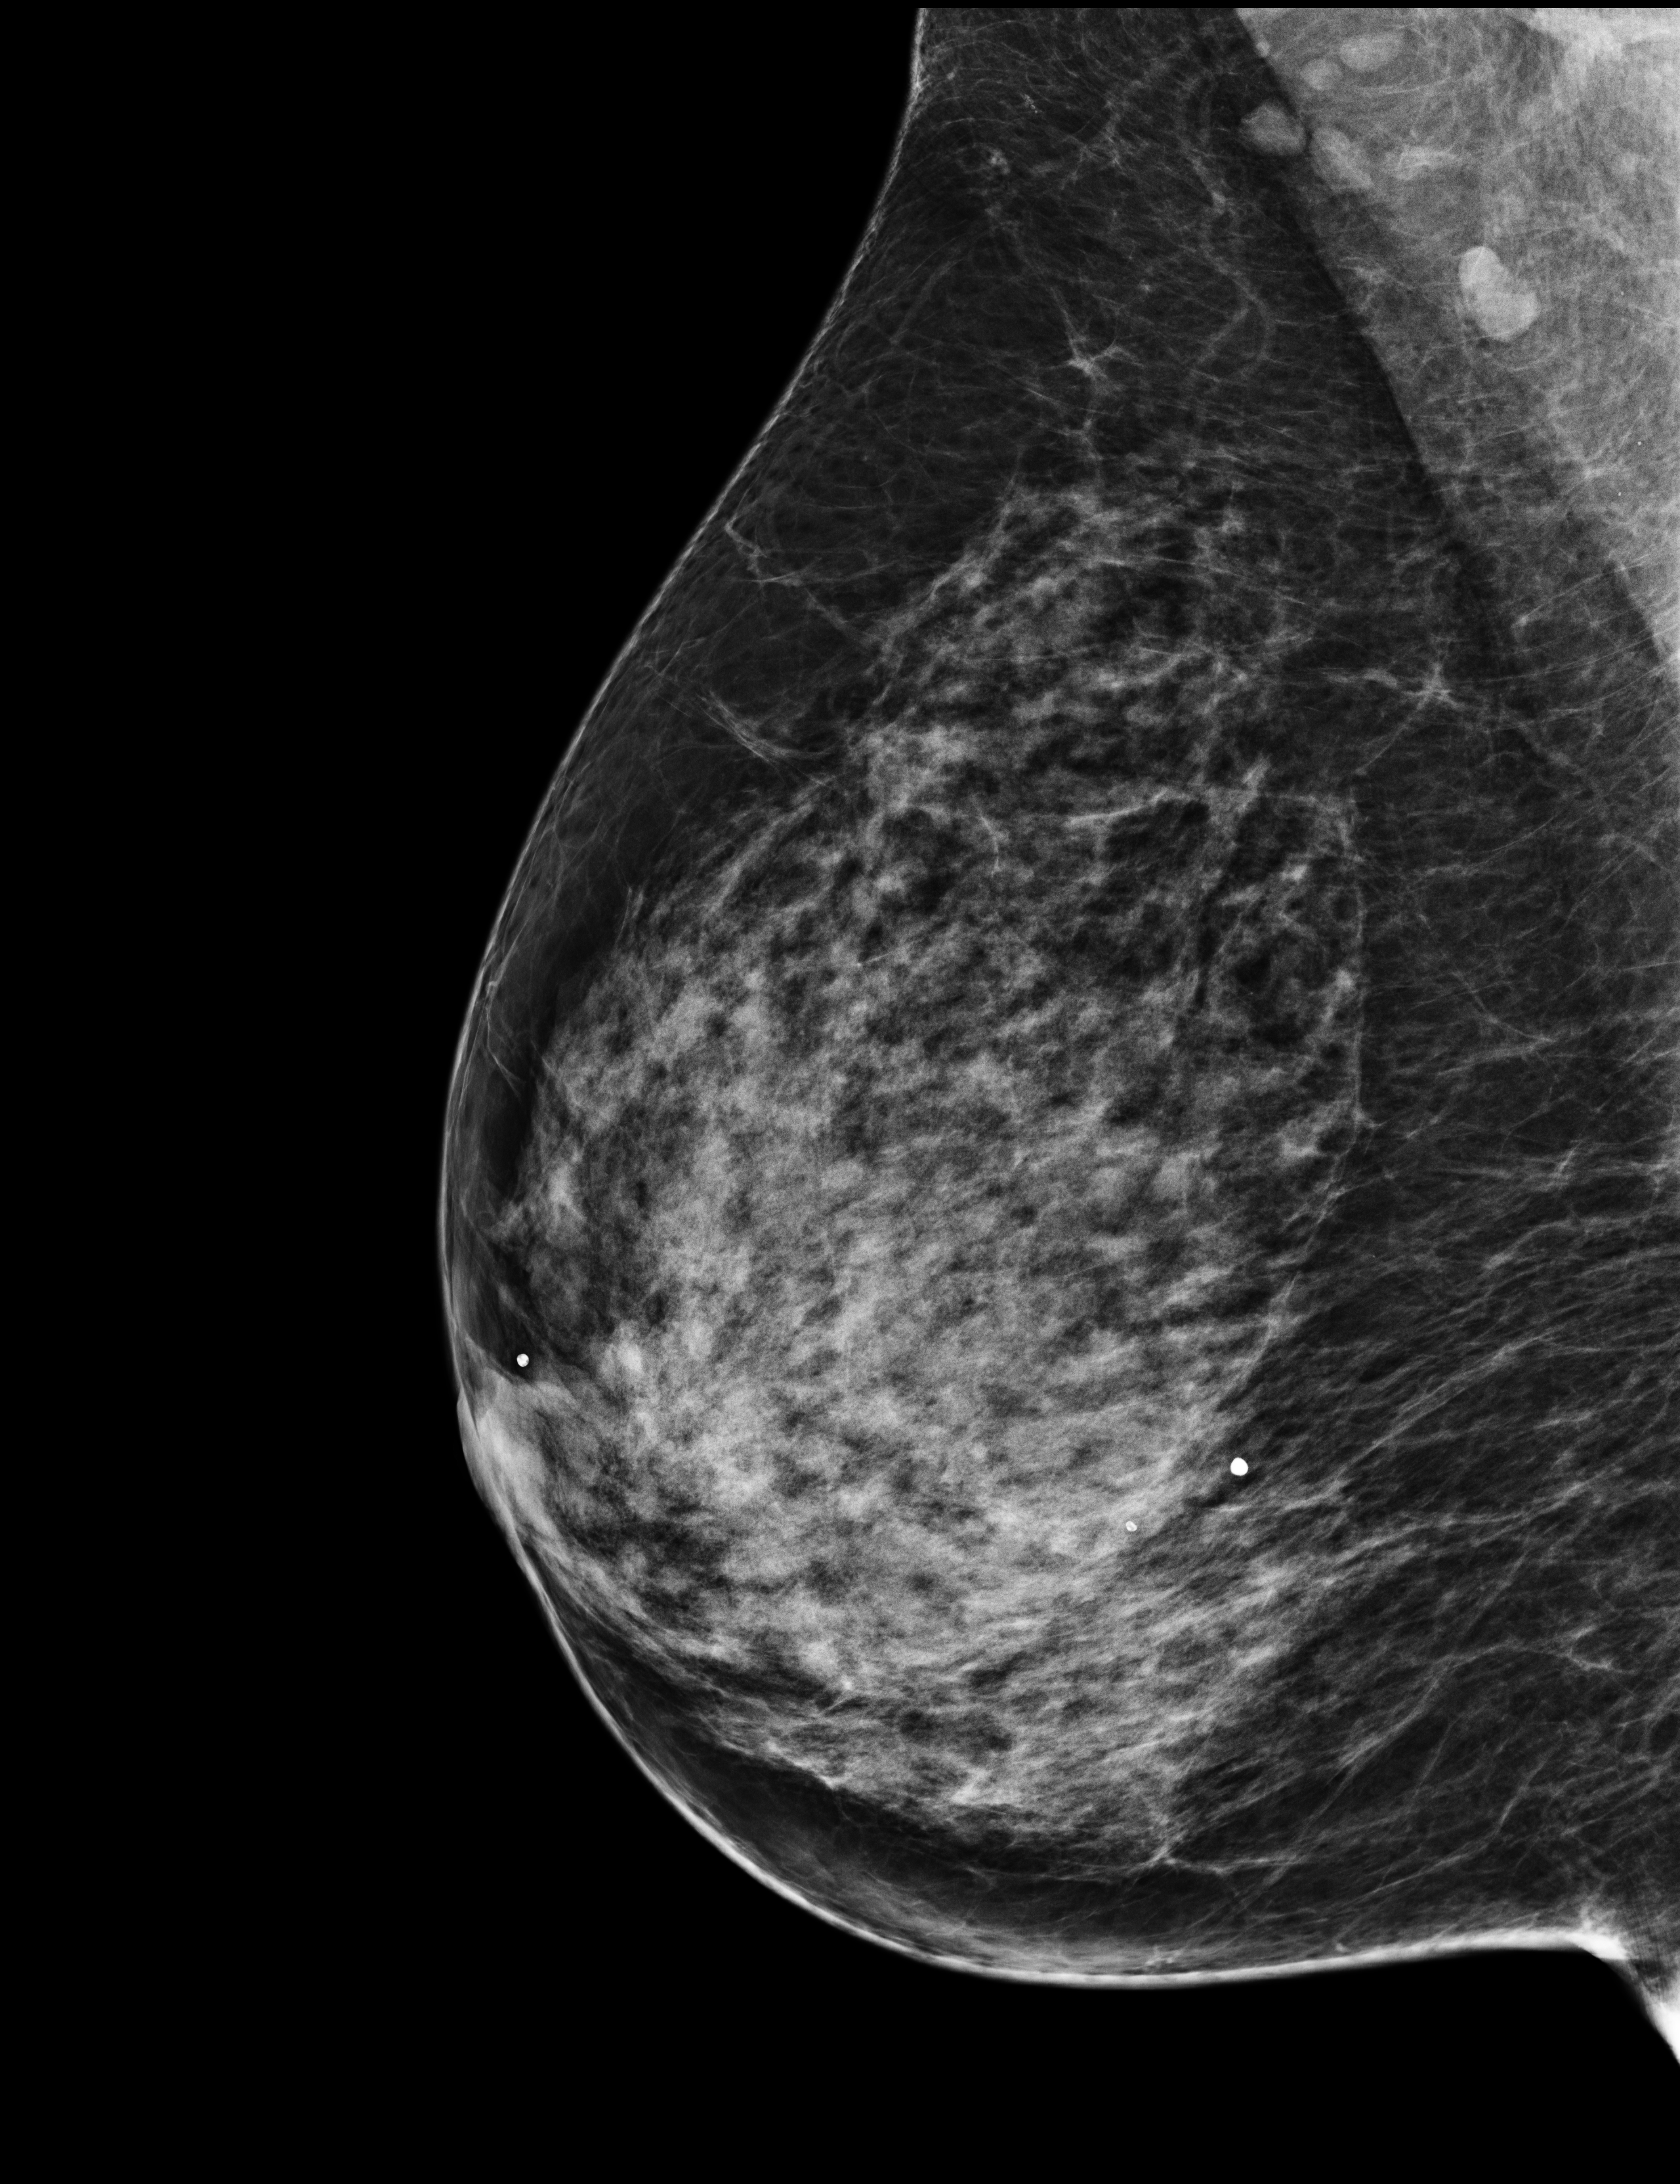
Digital mammogram (FFDM); right breast; medio-lateral oblique projection; screening examination; system: Selenia Dimensions. Patient aged 58 years (female).
Final BI-RADS assessment for this screening round (tomosynthesis exam, both breasts): category 1.